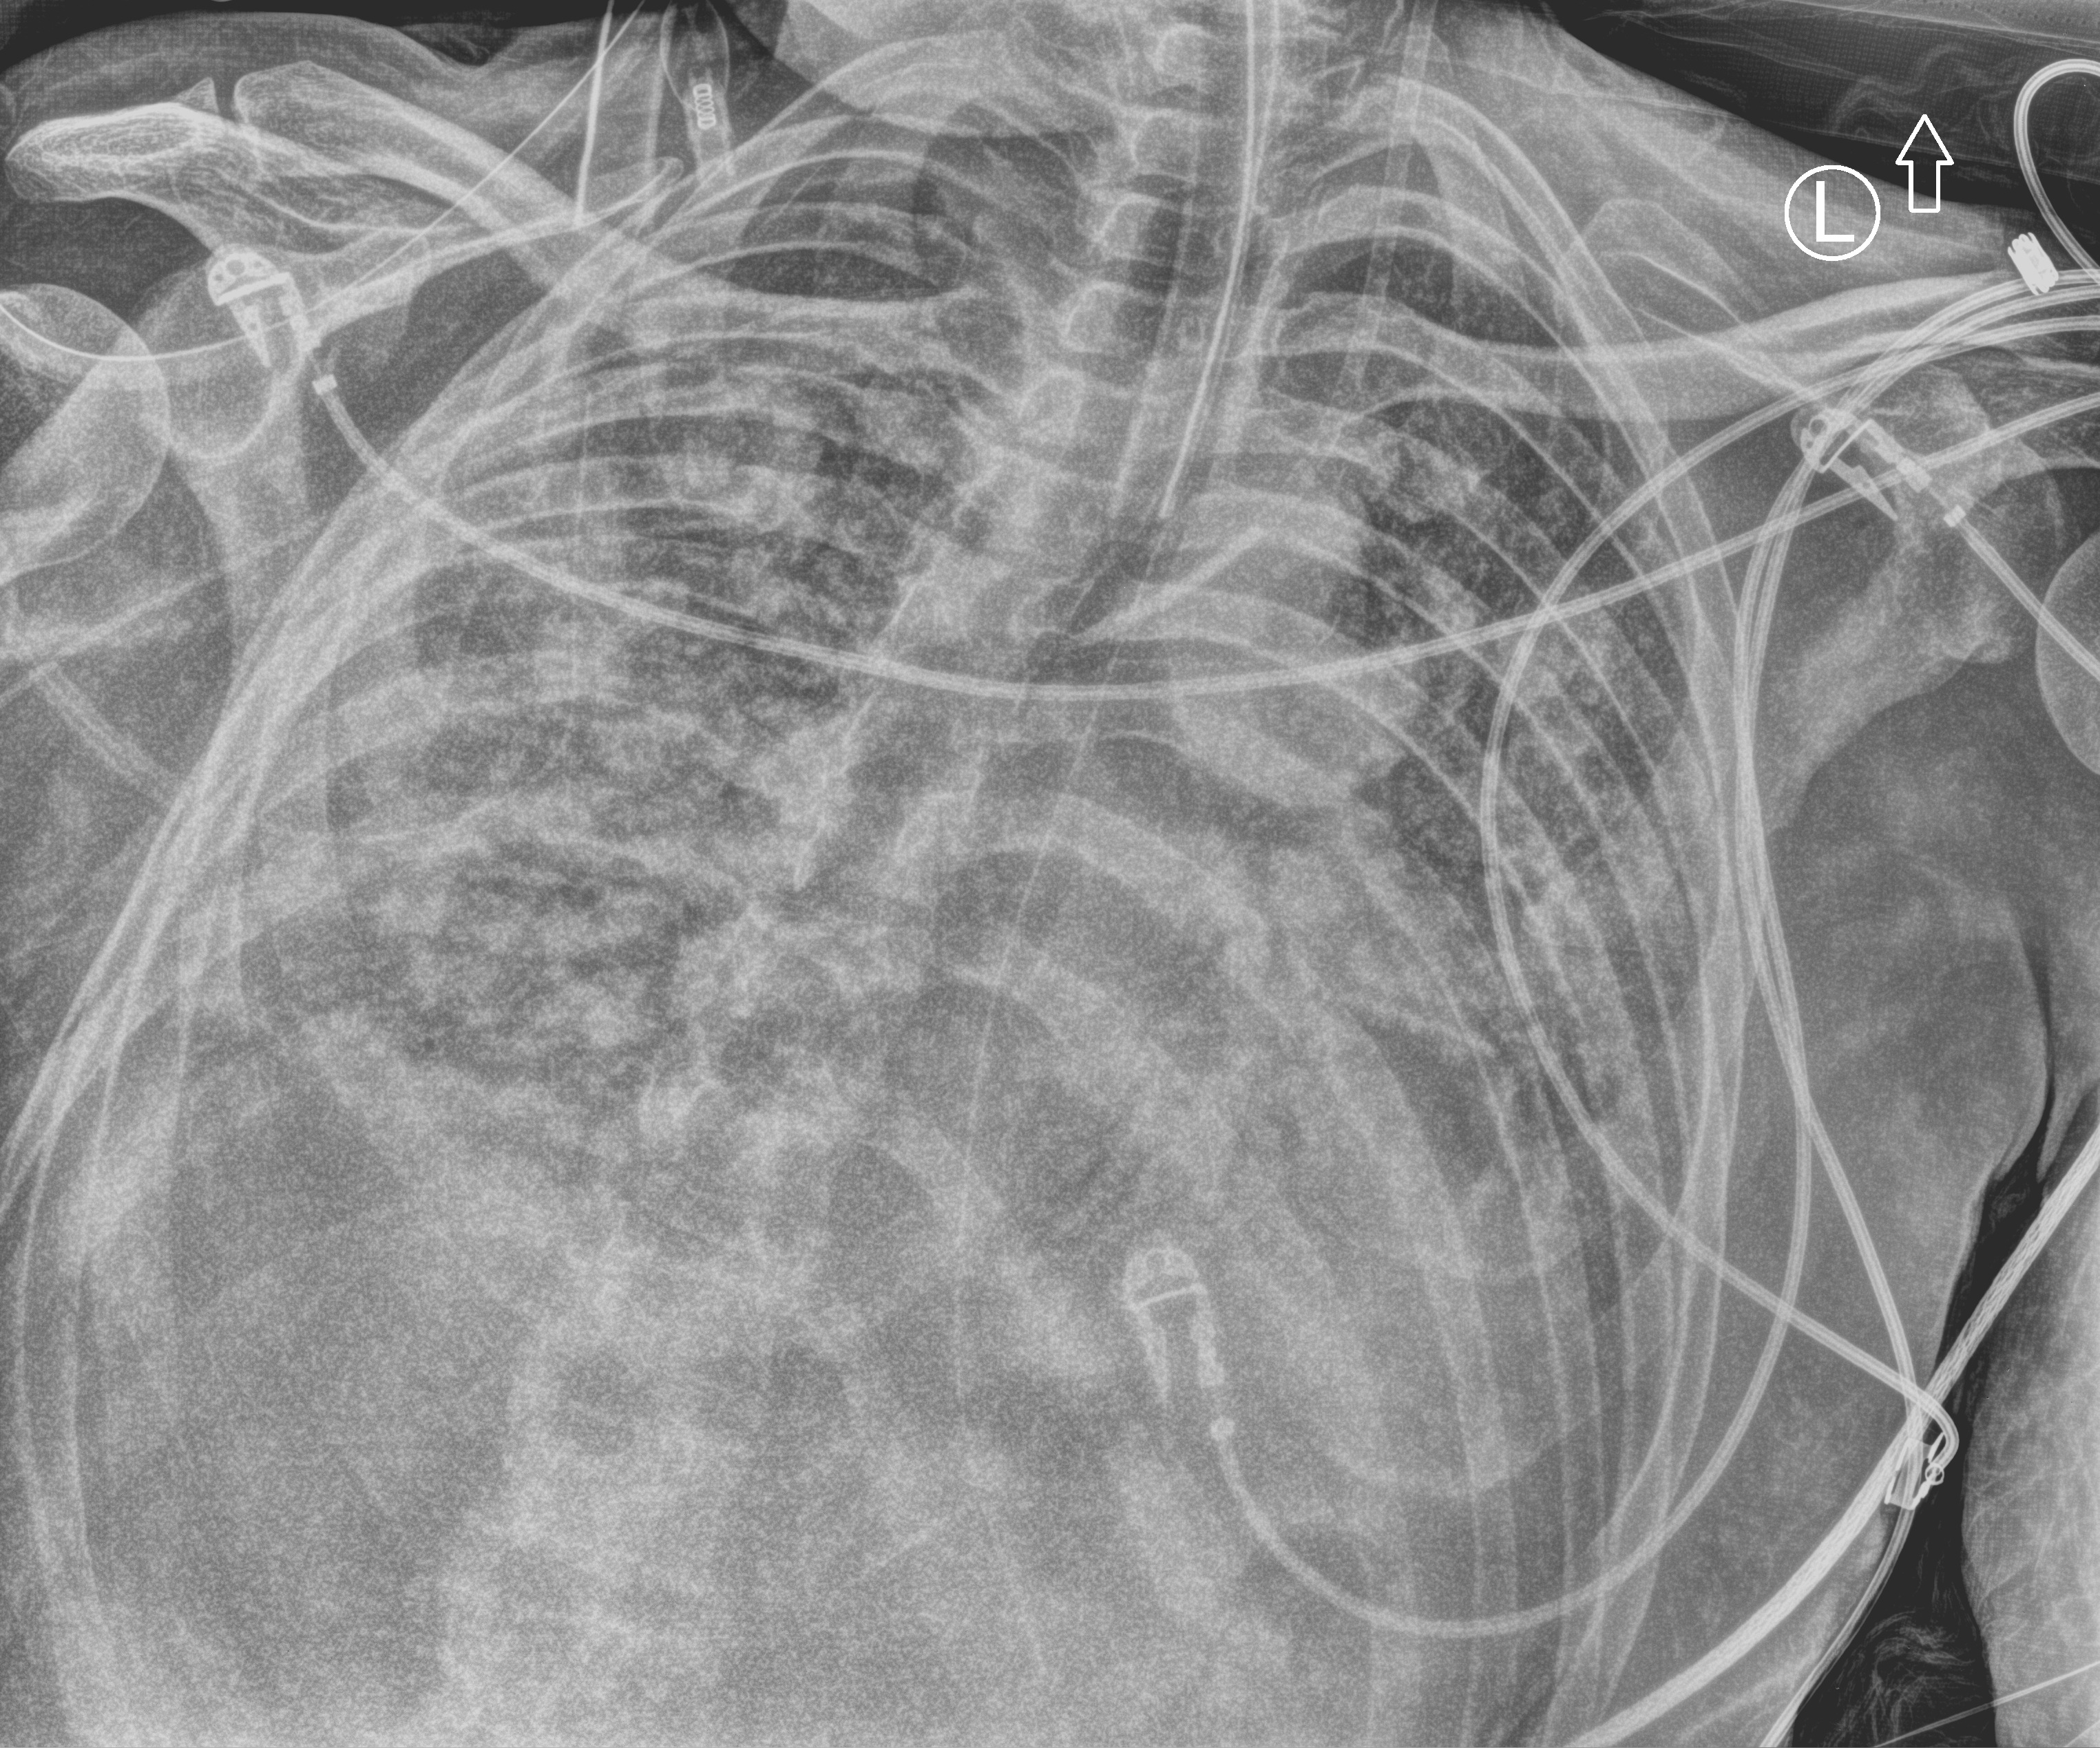
Chest X-ray (portable), anteroposterior (AP) projection. Male patient hospitalised with COVID-19, age 18–59 years.
Hospital-stay facts (about this admission, not read from this image; timing relative to this image not recorded): admitted to intensive care during this hospital stay: yes.